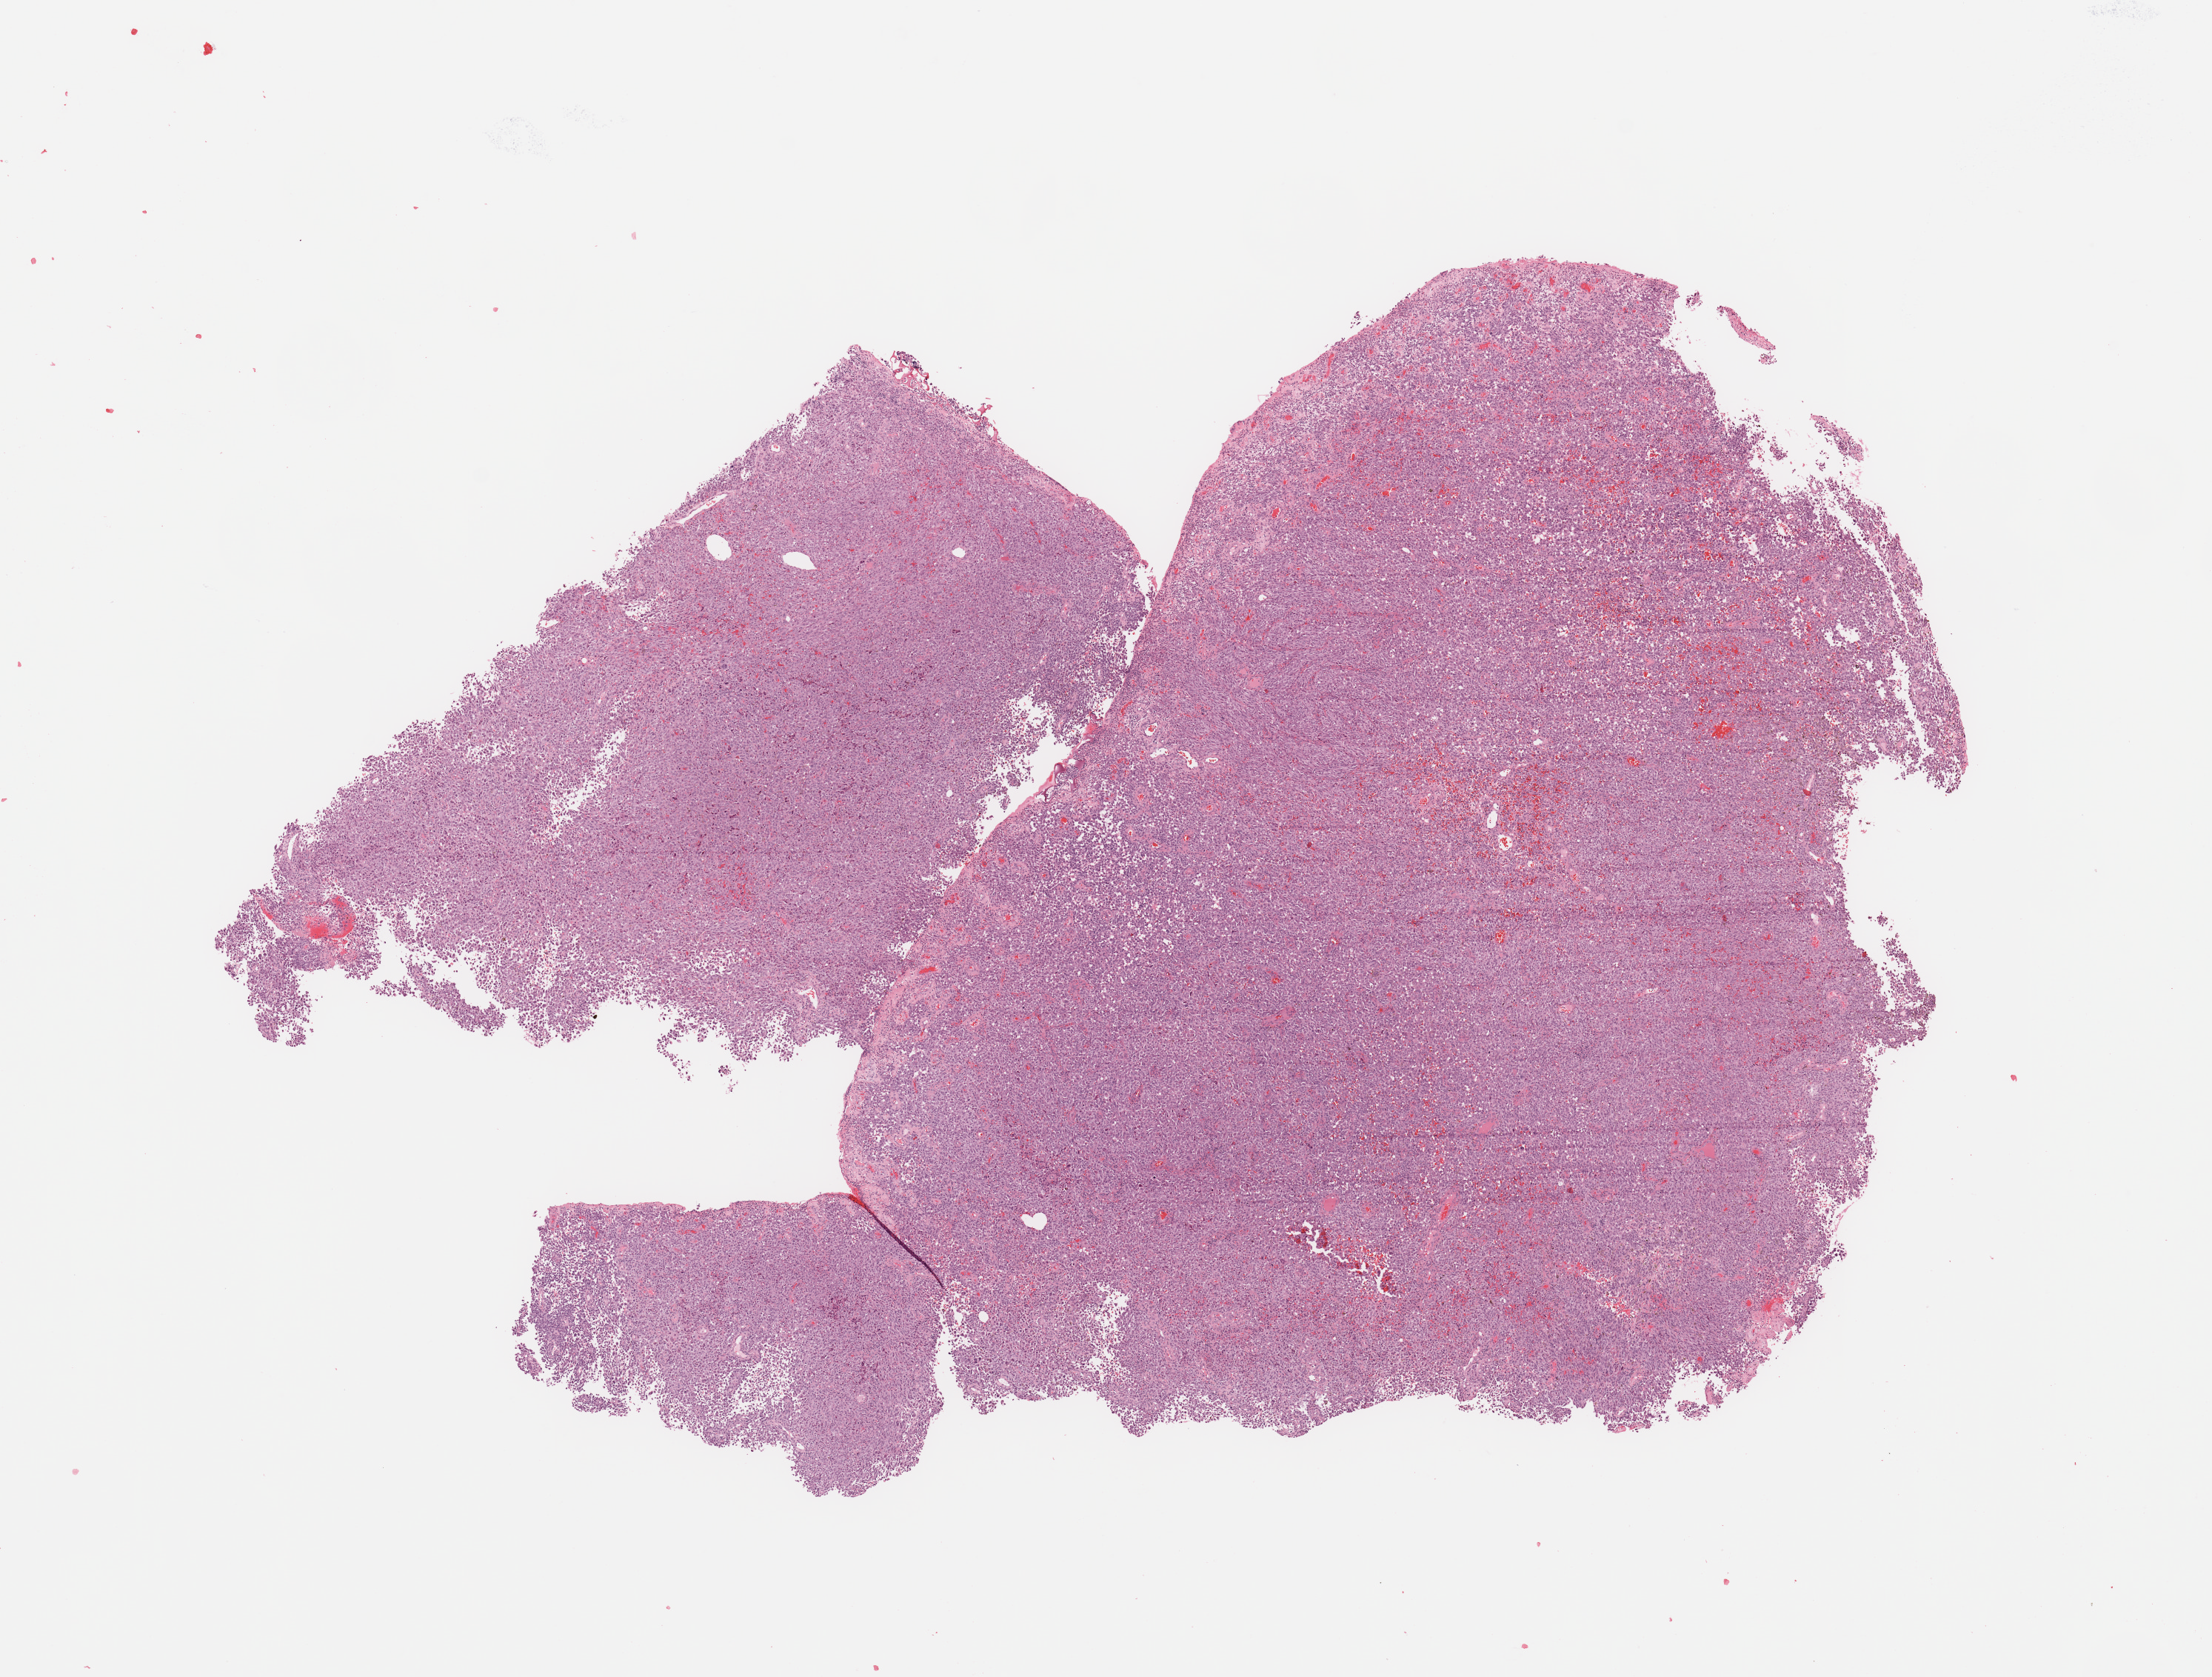
H&E-stained whole-slide image, shown as a low-resolution overview of the whole scanned area (about 11.8 x 9.0 mm, slide scanned at 20x), melanoma tumour tissue; sampled site not recorded. Patient: male, age 34 years.
AJCC pathologic stage: IIIB. Primary tumour site (as recorded): trunk. Histologic diagnosis: Malignant melanoma, NOS.